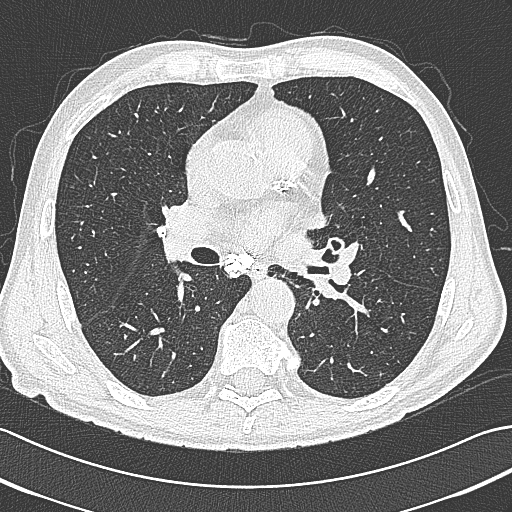
Axial slice from a low-dose chest CT screening exam, baseline annual screen, lung window (W 1500 / L -600 HU), 1 mm slice thickness, lung (sharp) reconstruction kernel (B80f), 512 × 512 image matrix, field of view 350 × 350 mm. Male, age 65 years at enrolment. Current smoker at enrolment.
• Expert reader's lesion annotation, bounding box [x1, y1, x2, y2] px = [305, 233, 355, 274].
• No non-calcified nodule or mass ≥4 mm was recorded by the screening reader at this exam.
• Official screen result: negative screen, minor abnormalities not suspicious for lung cancer.